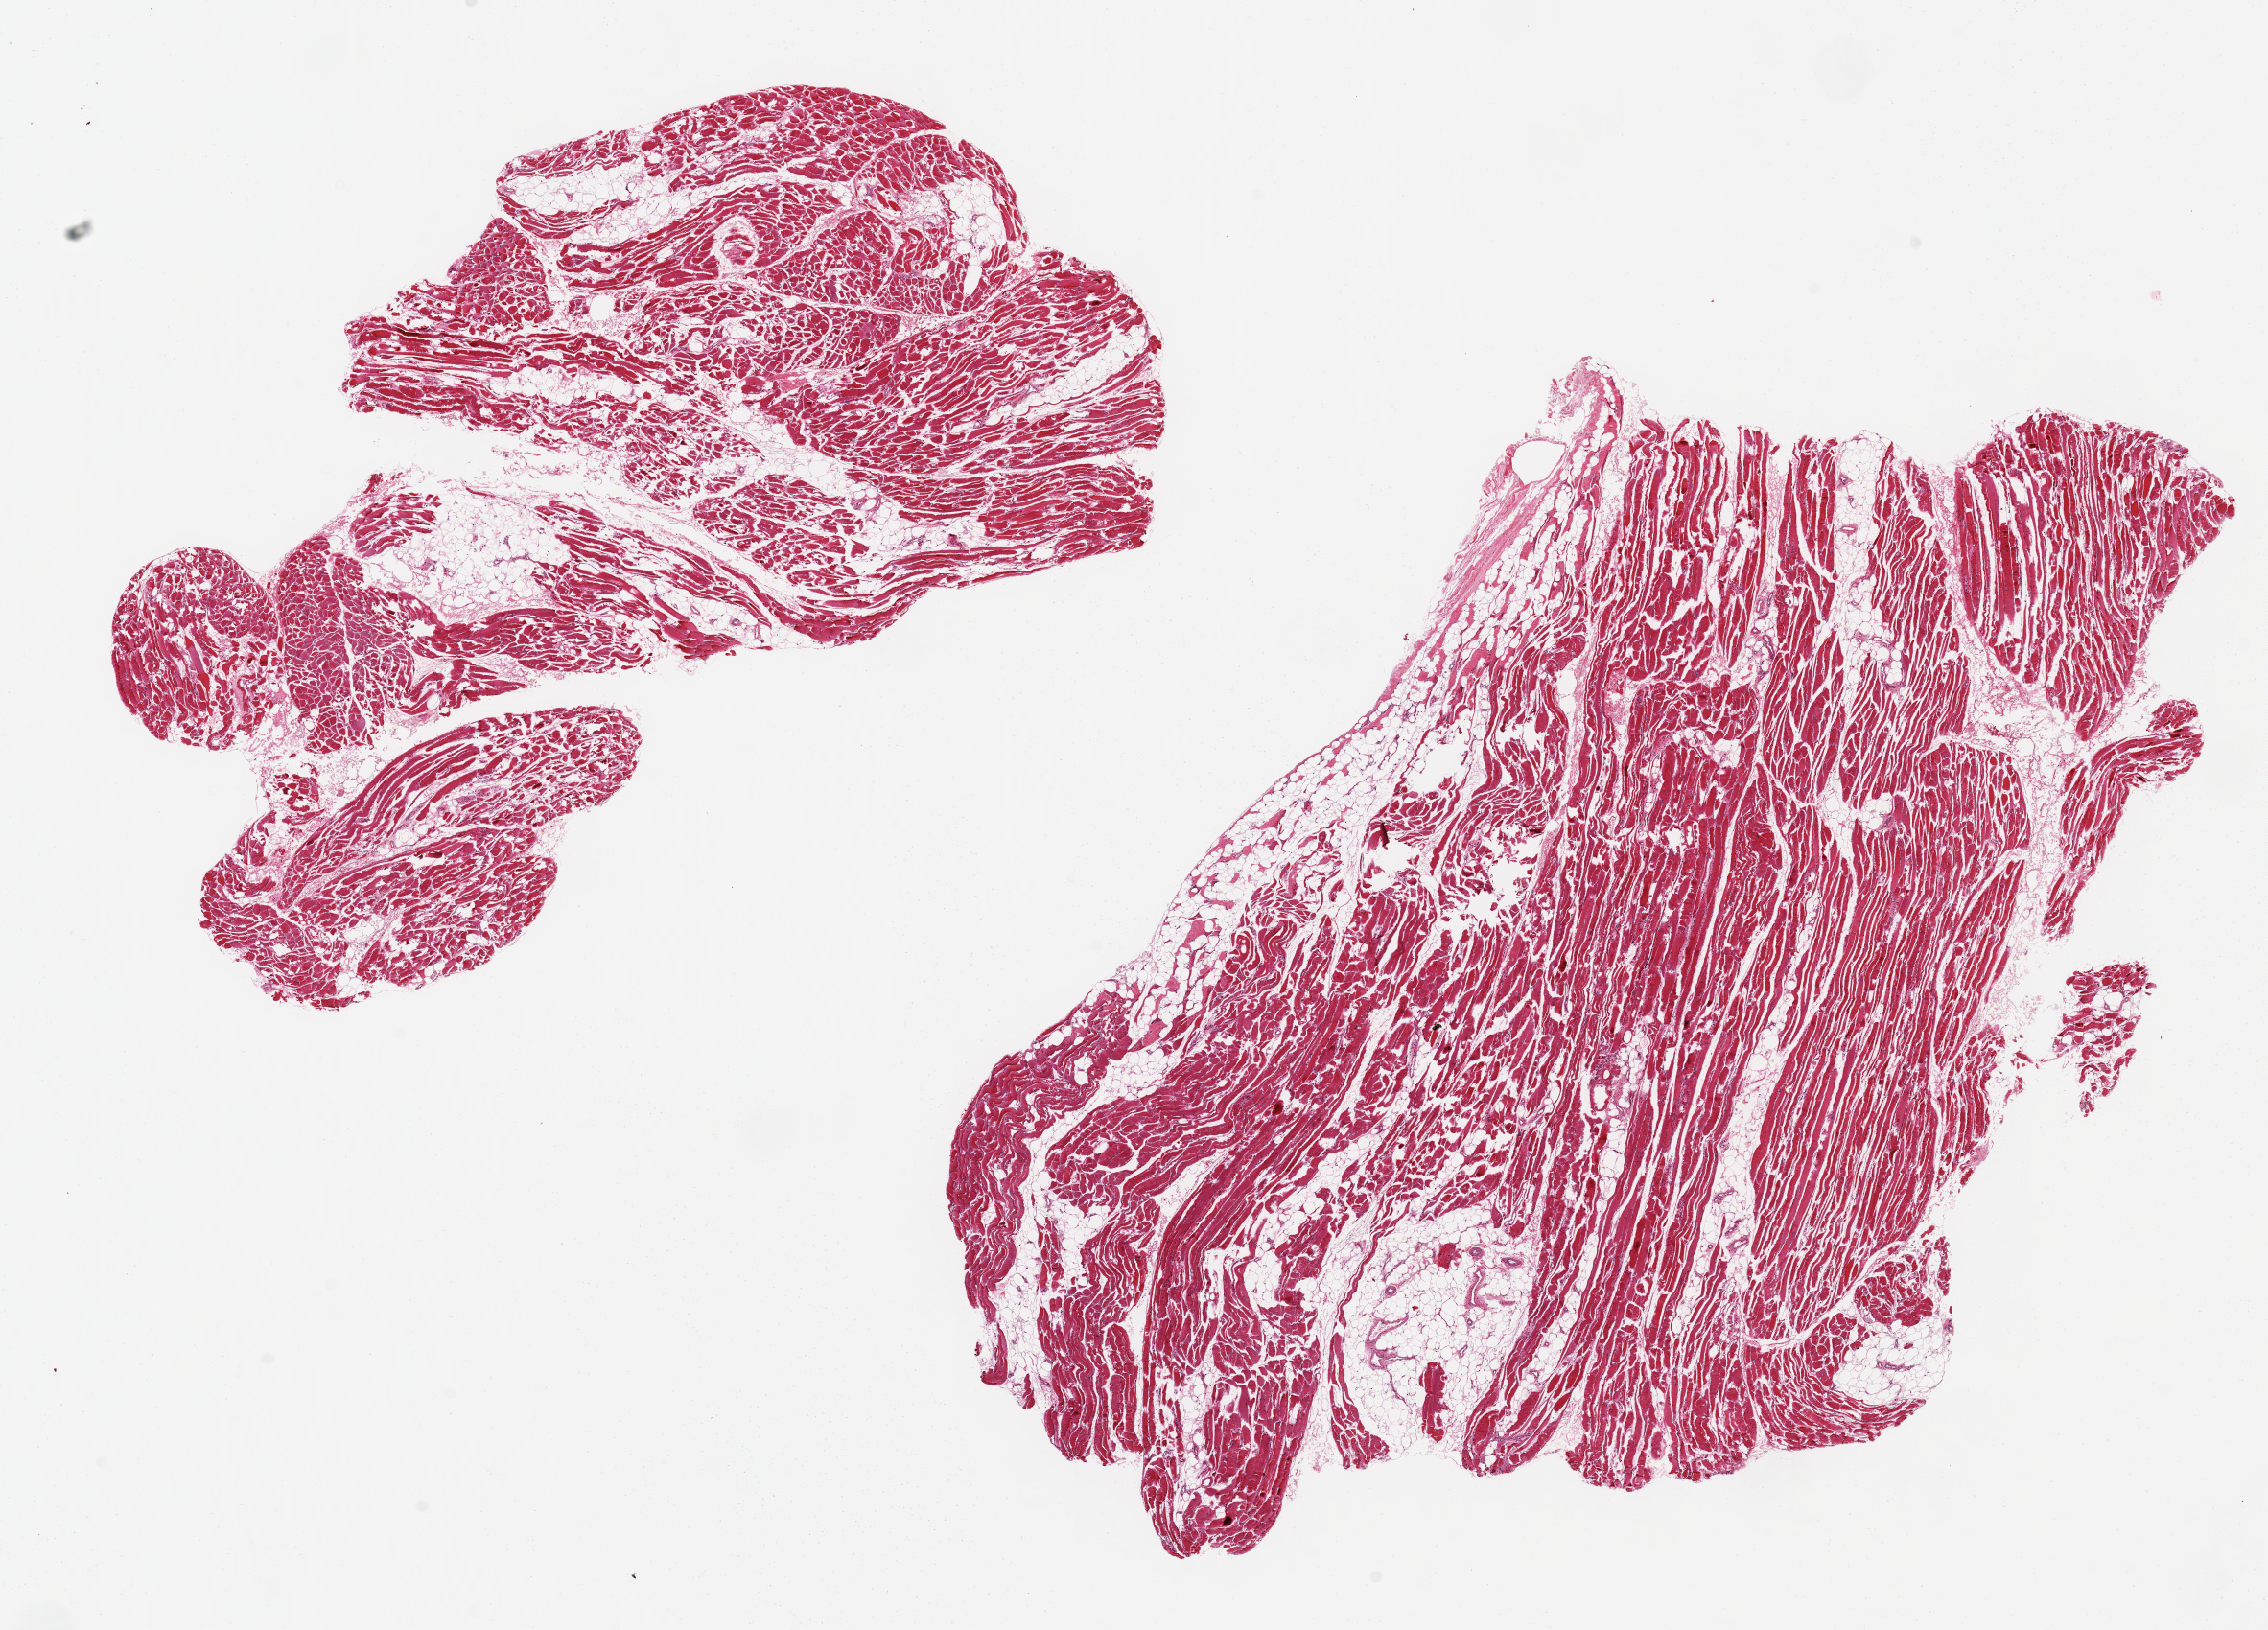
Digitized haematoxylin and eosin-stained section — low-resolution overview of the scanned area, about 18.7 x 13.4 mm (acquisition: 20x scan); PAXgene-fixed, paraffin-embedded tissue; sampled site (target tissue): skeletal muscle; tissue donor sample. Donor: male.
Pathologist's review note for this sample: 2 ~9x6mm aliquots, ~40% interstitial adipose tissue.